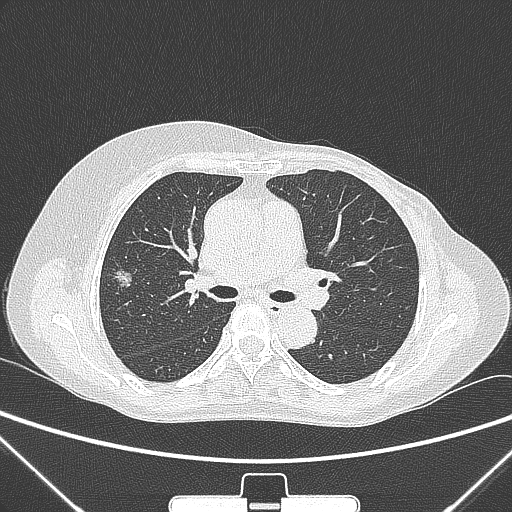
Chest CT, one axial slice; position 154 of 265 along the scan axis; 120 kVp; lung window (W 1500 / L -600 HU); 1 mm slice thickness; 512 × 512 image matrix, field of view 350 × 350 mm. Female patient, age 64 years. Case-level facts recorded for this patient, not image findings: clinical TNM (as recorded): T1c N0 M0; histopathological grade: G1-2.
Outlined on this slice (bounding box drawn by a radiologist):
- lung tumour (recorded histology: adenocarcinoma): box from (x=107, y=266) to (x=137, y=292) px